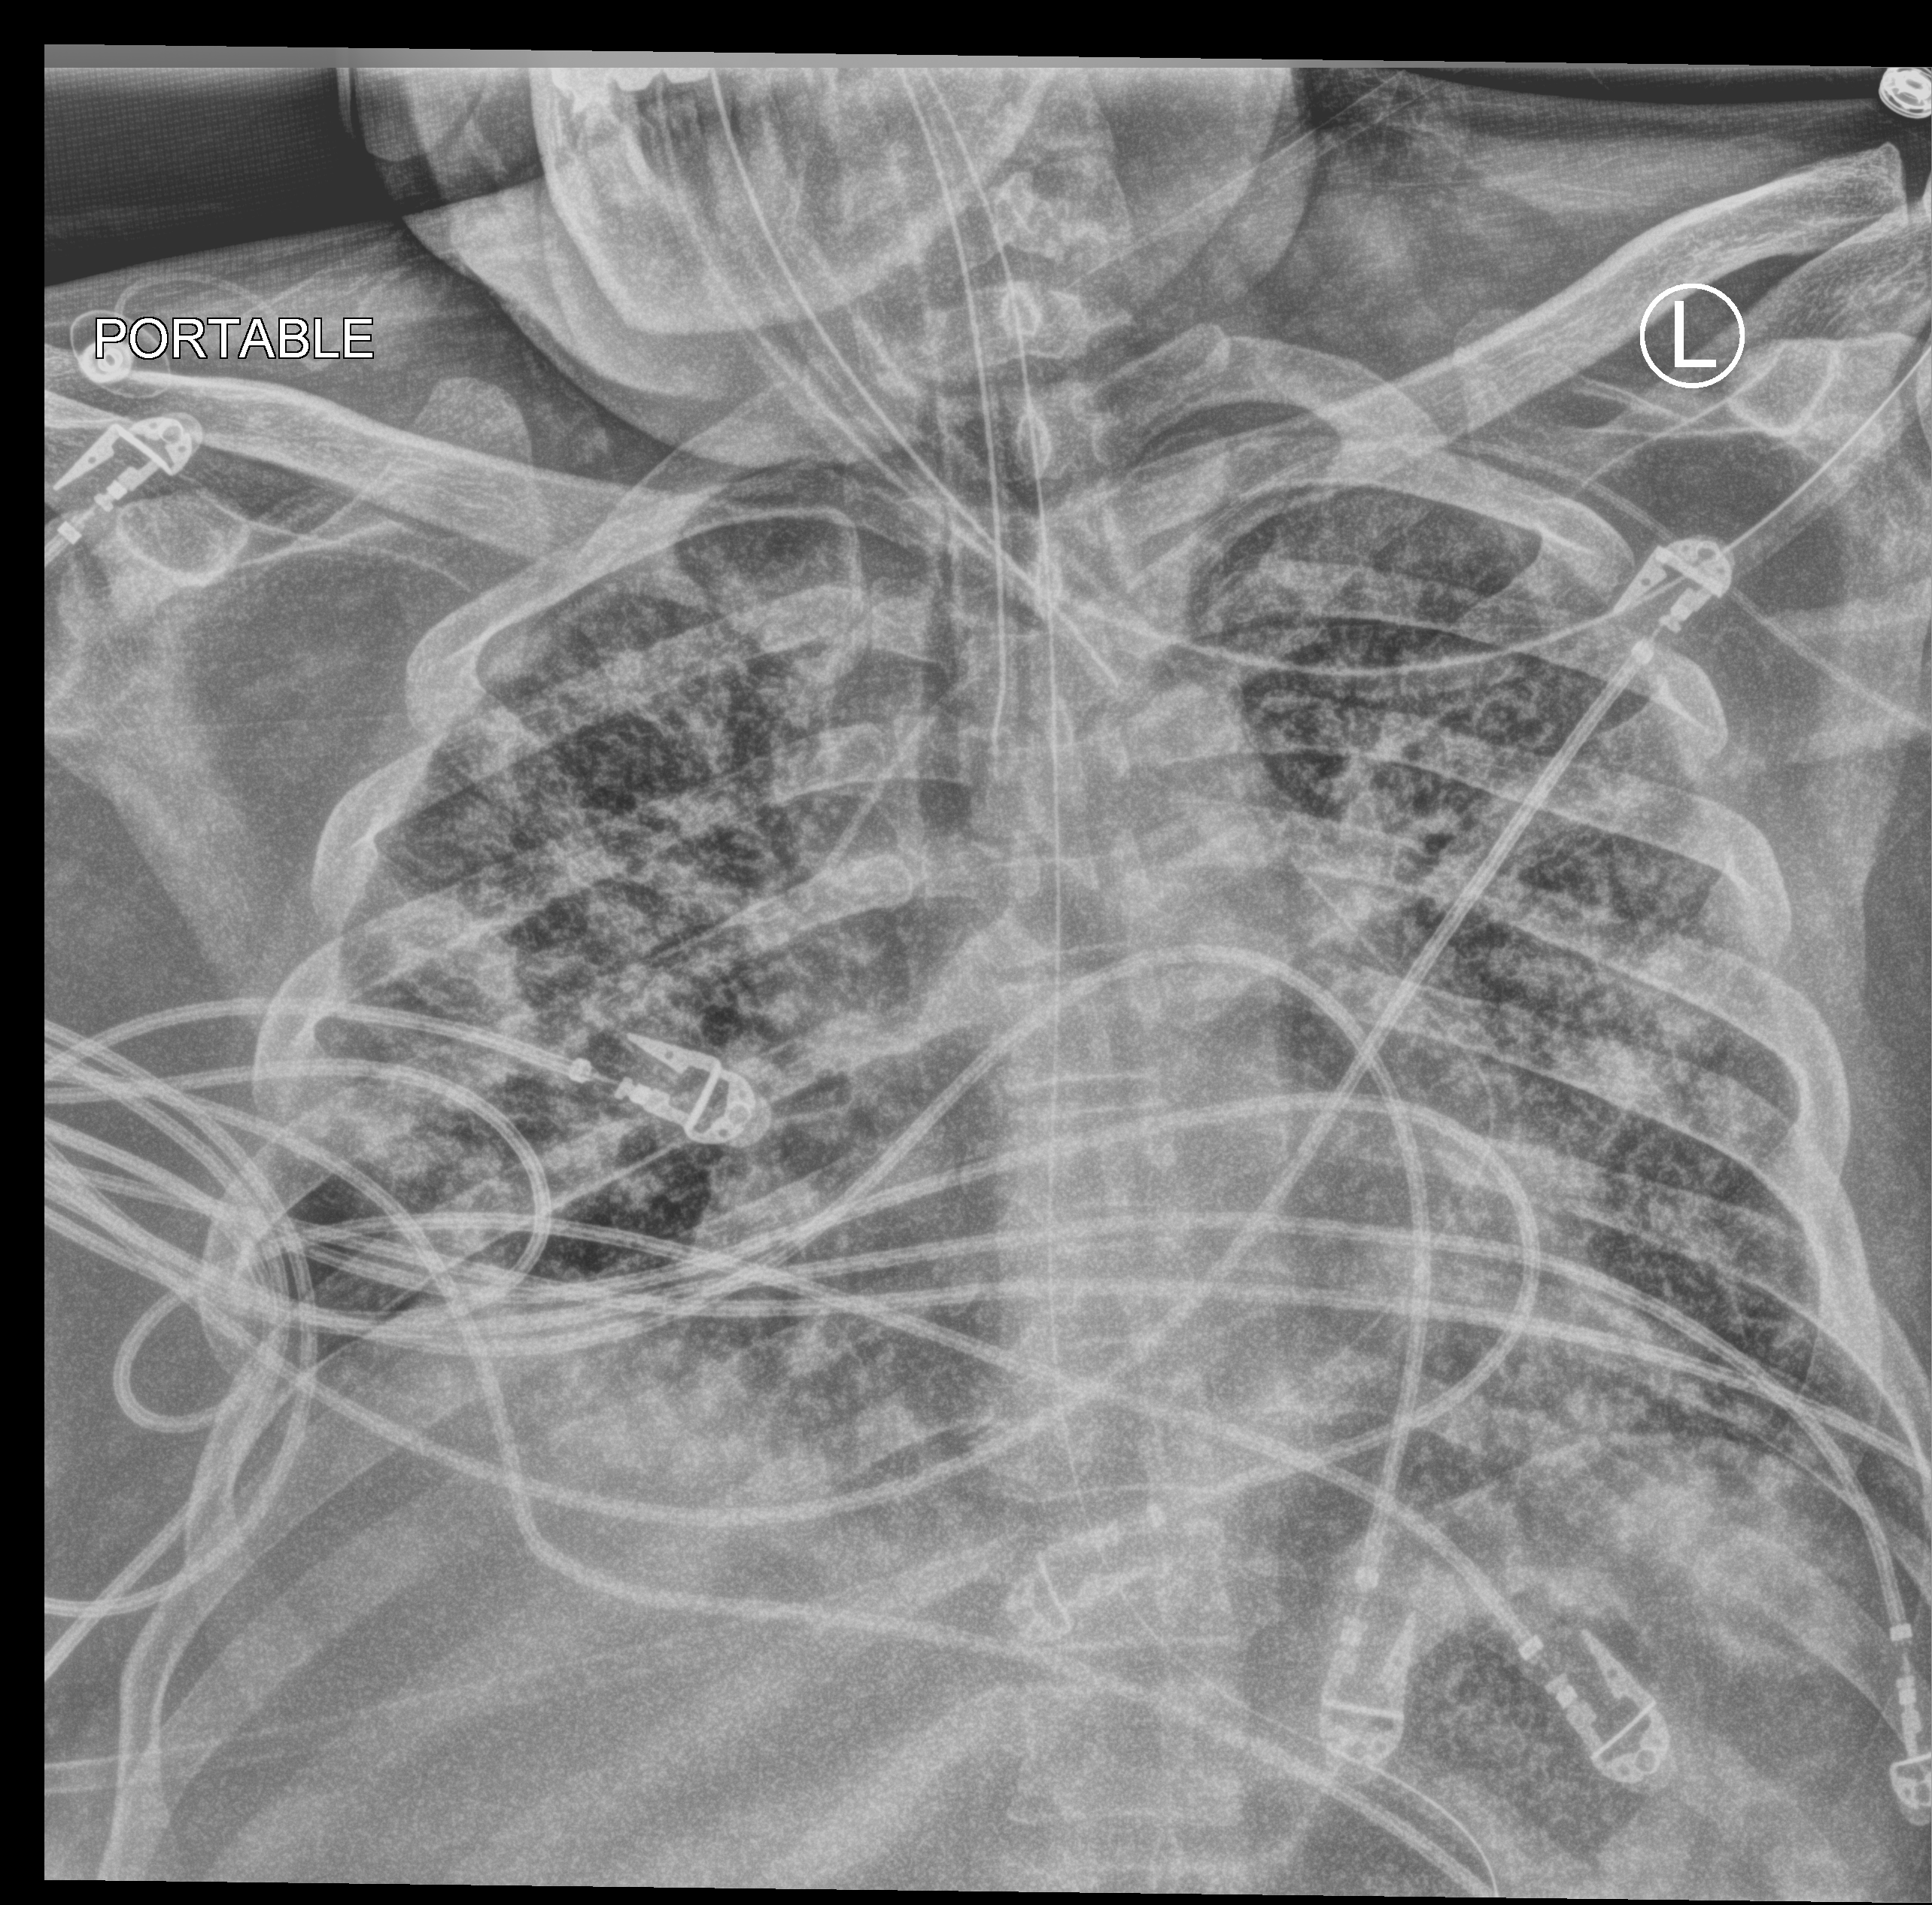
Portable chest radiograph, anteroposterior (AP) projection. Patient hospitalised with COVID-19; male, aged 18–59 years.
Hospital-stay facts (about this admission, not read from this image; timing relative to this image not recorded): mechanically ventilated during this hospital stay: yes.